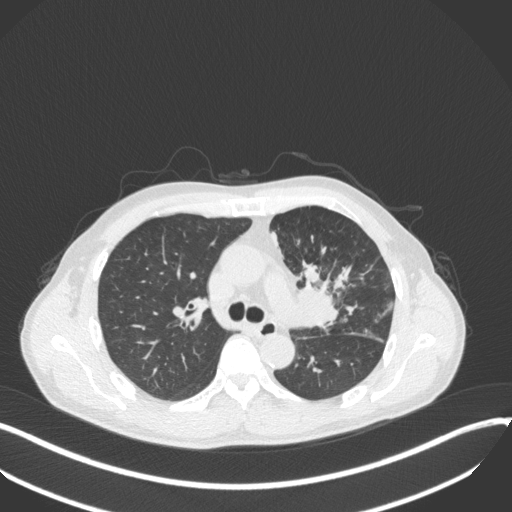
Chest CT, one axial slice. Position 222 of 411 along the scan axis. Lung window (W 1500 / L -600 HU). 1 mm slice thickness. 512 × 512 image matrix, field of view 400 × 400 mm. Patient: male, 56 years. From the clinical record (not read from this slice): clinical TNM (as recorded): T2a N0 M0.
Structures marked on this image (rectangle marked by the reading radiologist):
- lung tumour (recorded histology: squamous cell carcinoma): bounding box <294,260,349,329> (left, top, right, bottom; pixels)